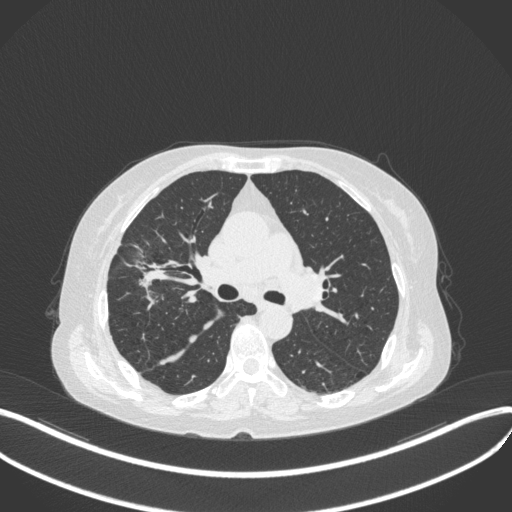
Chest CT, one axial slice. Slice 247 of 429 in the series (ordered by position). Reconstruction kernel B31f. Lung window (W 1500 / L -600 HU). 1 mm slice thickness. 512 × 512 image matrix, field of view 400 × 400 mm. Female patient, age 69 years. Case-level facts recorded for this patient, not image findings: clinical TNM (as recorded): T1b N3 M0.
Annotated regions visible in this slice (bounding box drawn by a radiologist):
- lung tumour (recorded histology: small cell carcinoma): bounding box [x1, y1, x2, y2] px = [125, 243, 170, 300]